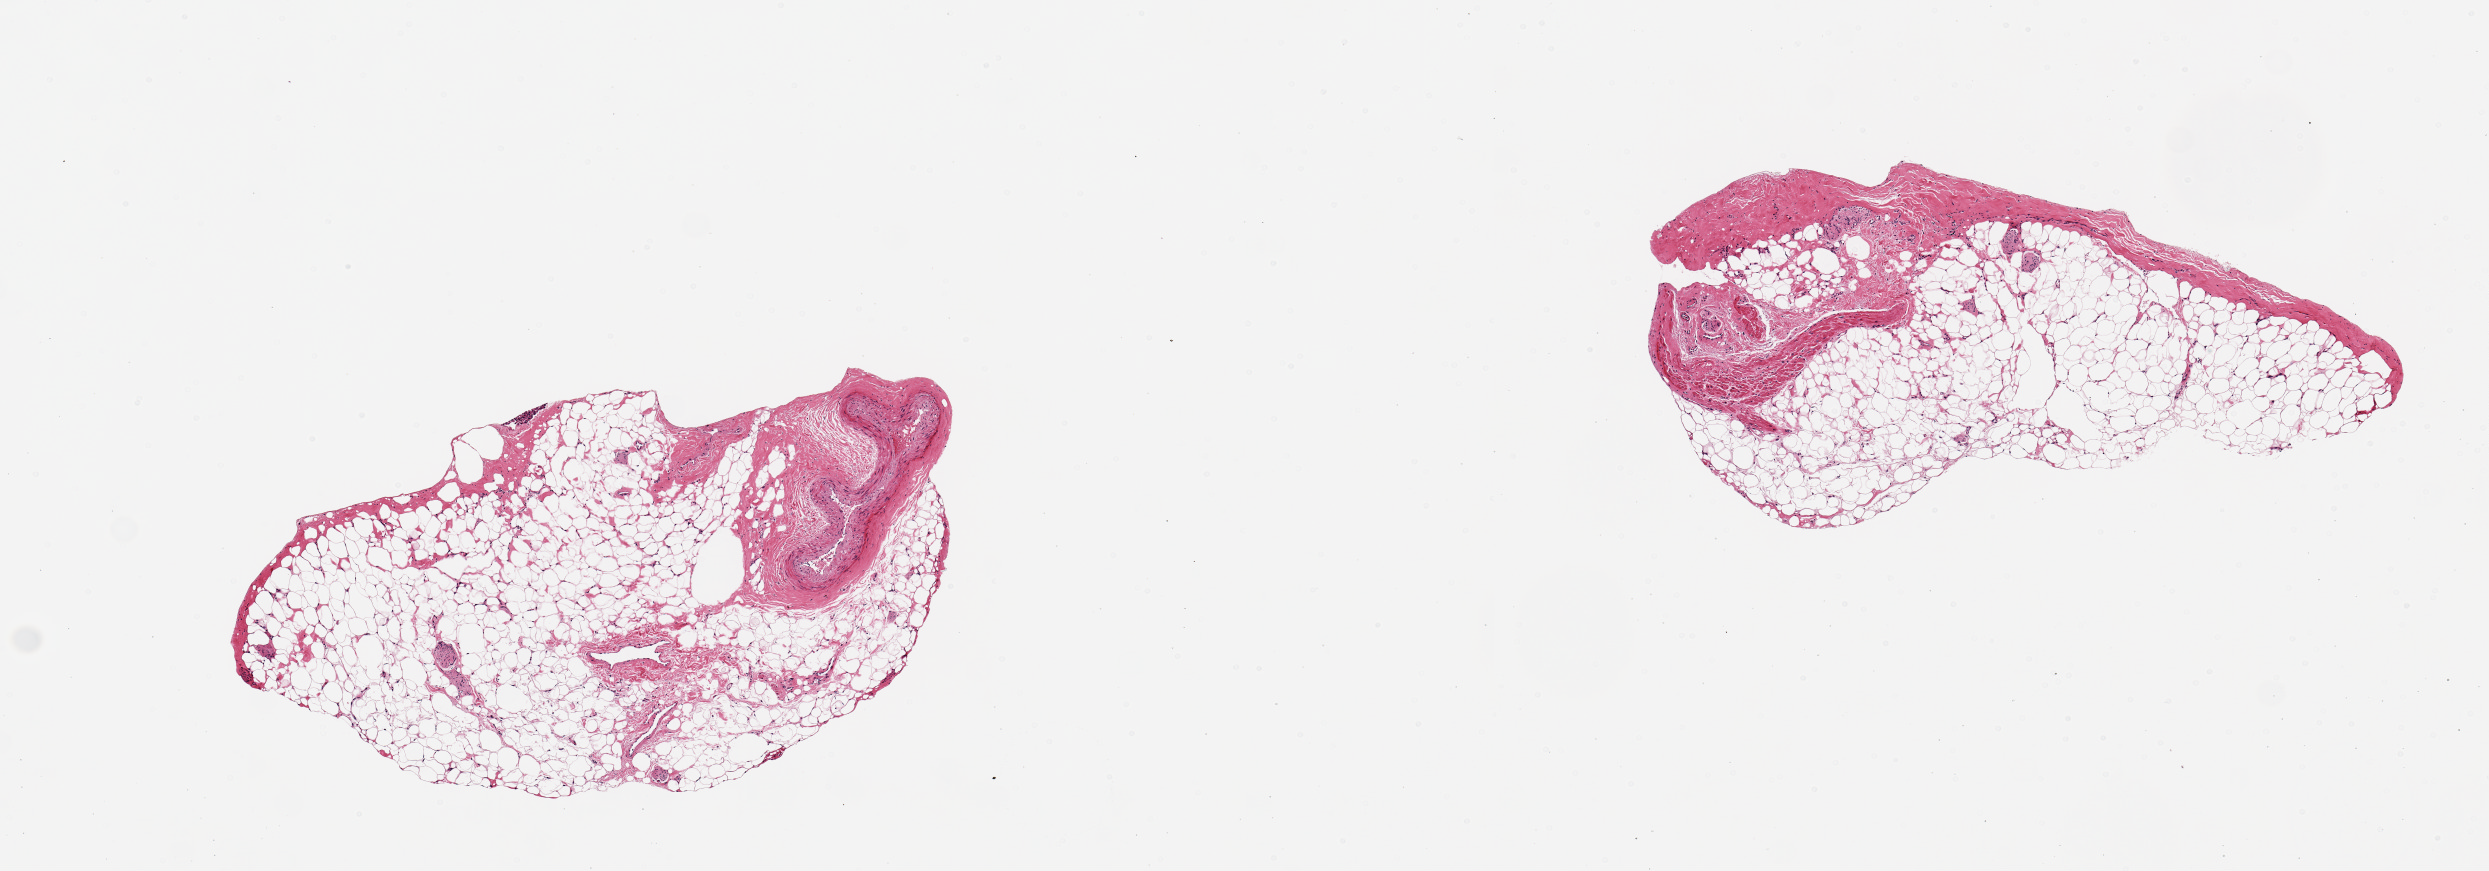
H&E whole-slide image, brightfield, a low-resolution overview of the entire scanned area, about 9.8 x 3.4 mm (acquisition: 20x scan). PAXgene-fixed, paraffin-embedded tissue. Sampled site (target tissue): coronary artery. Tissue donor sample. Female donor.
Reviewer comment on this tissue sample: 2 aliquots ~3 x 1.5mm. Only one has a ~0.66mm coronary artery section; the rest is adipose tissue; artery is less than 10% of total tissue area.